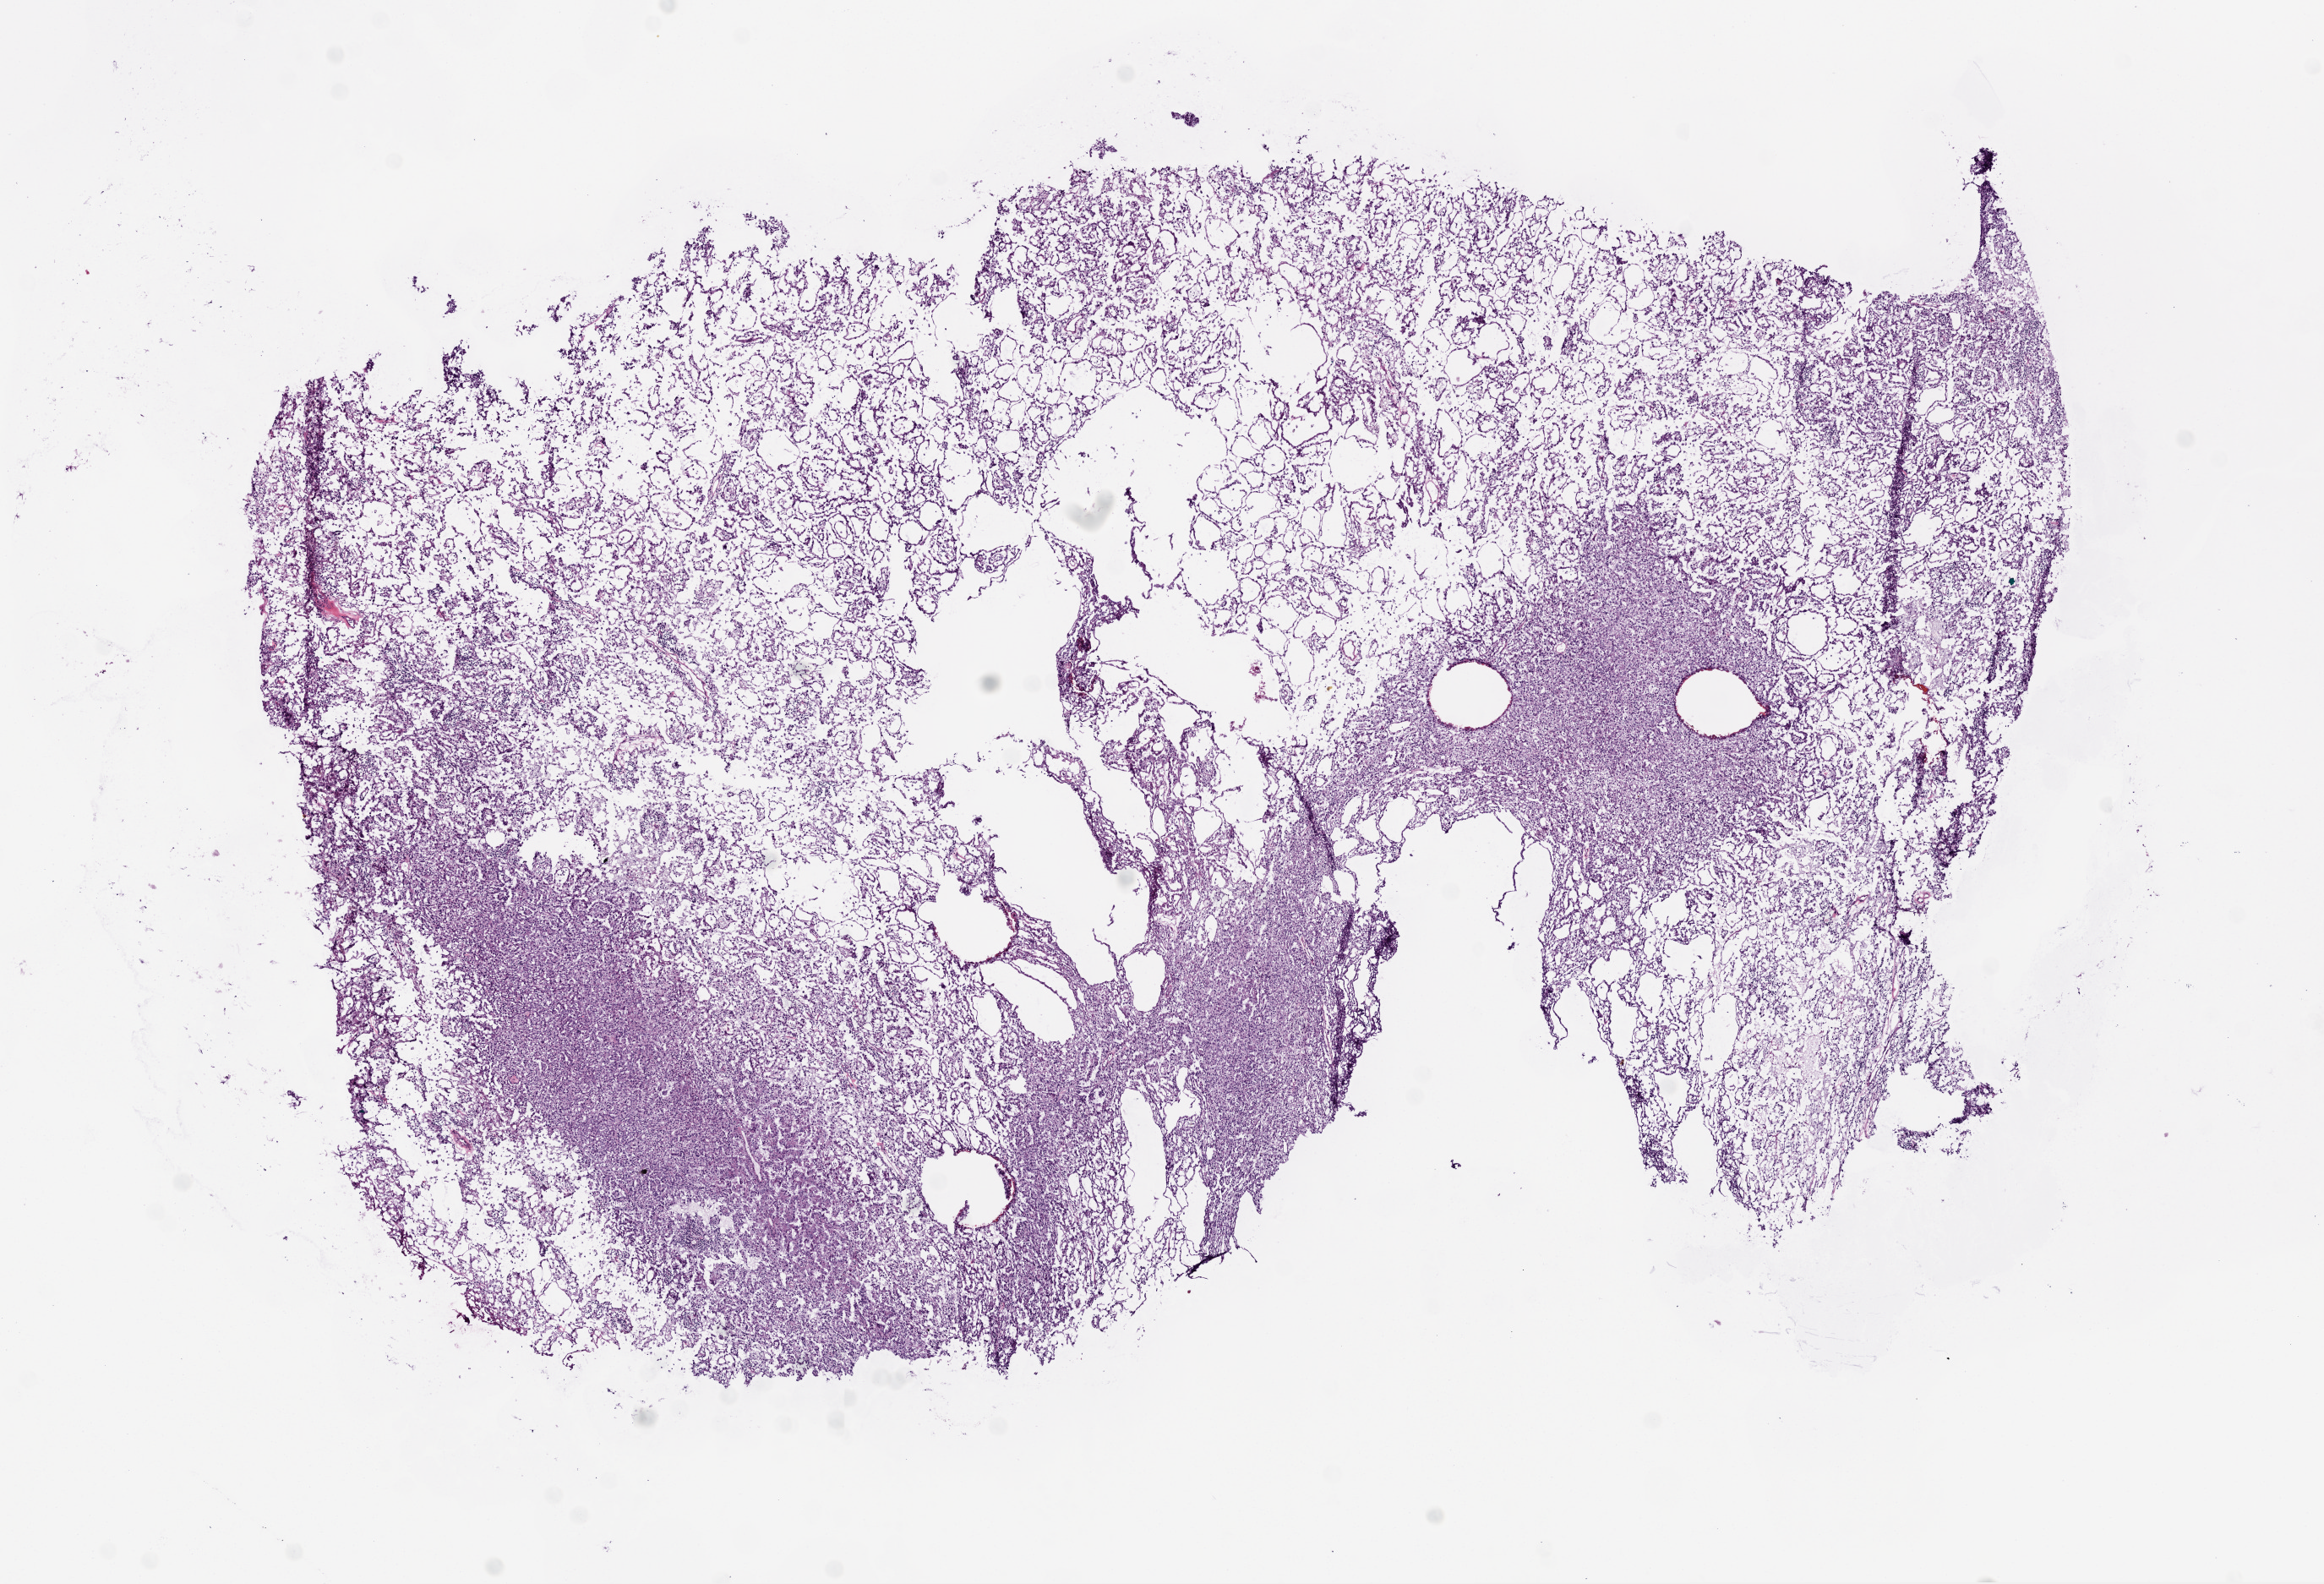
Whole-slide histology image, H&E-stained — shown as a low-resolution overview of the whole scanned area (about 11.0 x 7.5 mm, acquisition: 20x scan), frozen section from the top of the tissue portion, sample: primary tumour, kidney. Female patient; age at initial diagnosis 61 years. Composition of this section per pathologist review: tumour cells 95%, tumour nuclei 80%, normal cells 0%, stromal cells 5%, necrosis 0%.
Pathologic diagnosis: Papillary adenocarcinoma, NOS. AJCC pathologic stage: I (7th edition).